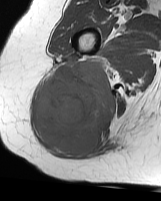
MRI of an extremity soft-tissue mass, one axial slice. Slice 35 of 70 in the series (ordered by position). MR volume resampled by the dataset authors to the PET/CT grid (not the native acquisition matrix). 3.27 mm slice thickness. 161 × 201 image matrix, field of view 157 × 196 mm. Female patient. Case-level facts recorded for this patient, not image findings: histological type: synovial sarcoma; grade: intermediate; site of the primary tumour: right buttock.
Structures marked on this image (expert contour drawn on MRI and transferred to this co-registered scan by the dataset authors):
- gross tumour volume including surrounding oedema: box from (x=35, y=58) to (x=116, y=155) px
- gross tumour volume (mass): (x=35, y=59)–(x=116, y=155)